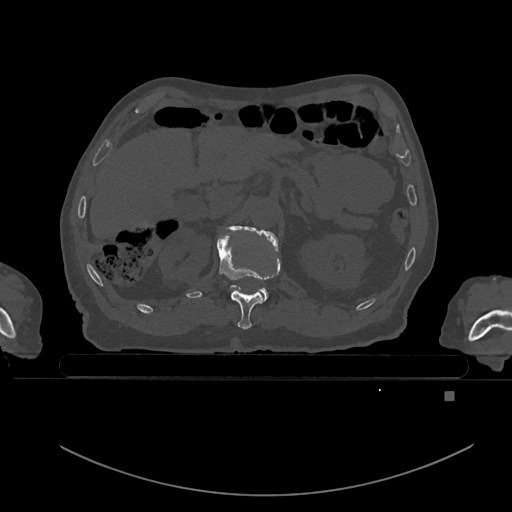
CT including the spine, one axial slice; position 2 of 969 along the scan axis; bone window (W 1800 / L 400 HU); 0.5 mm slice thickness; 512 × 512 image matrix. Patient: male, 82 years. From the clinical record (not read from this slice): primary cancer: prostate; vertebrae with lytic lesions (as recorded): T11, T9, T8, T2.
Annotated regions visible in this slice (semi-automatic segmentation, software-assisted and operator-edited):
- T11 vertebra: bounding box <217,227,278,329> (left, top, right, bottom; pixels)